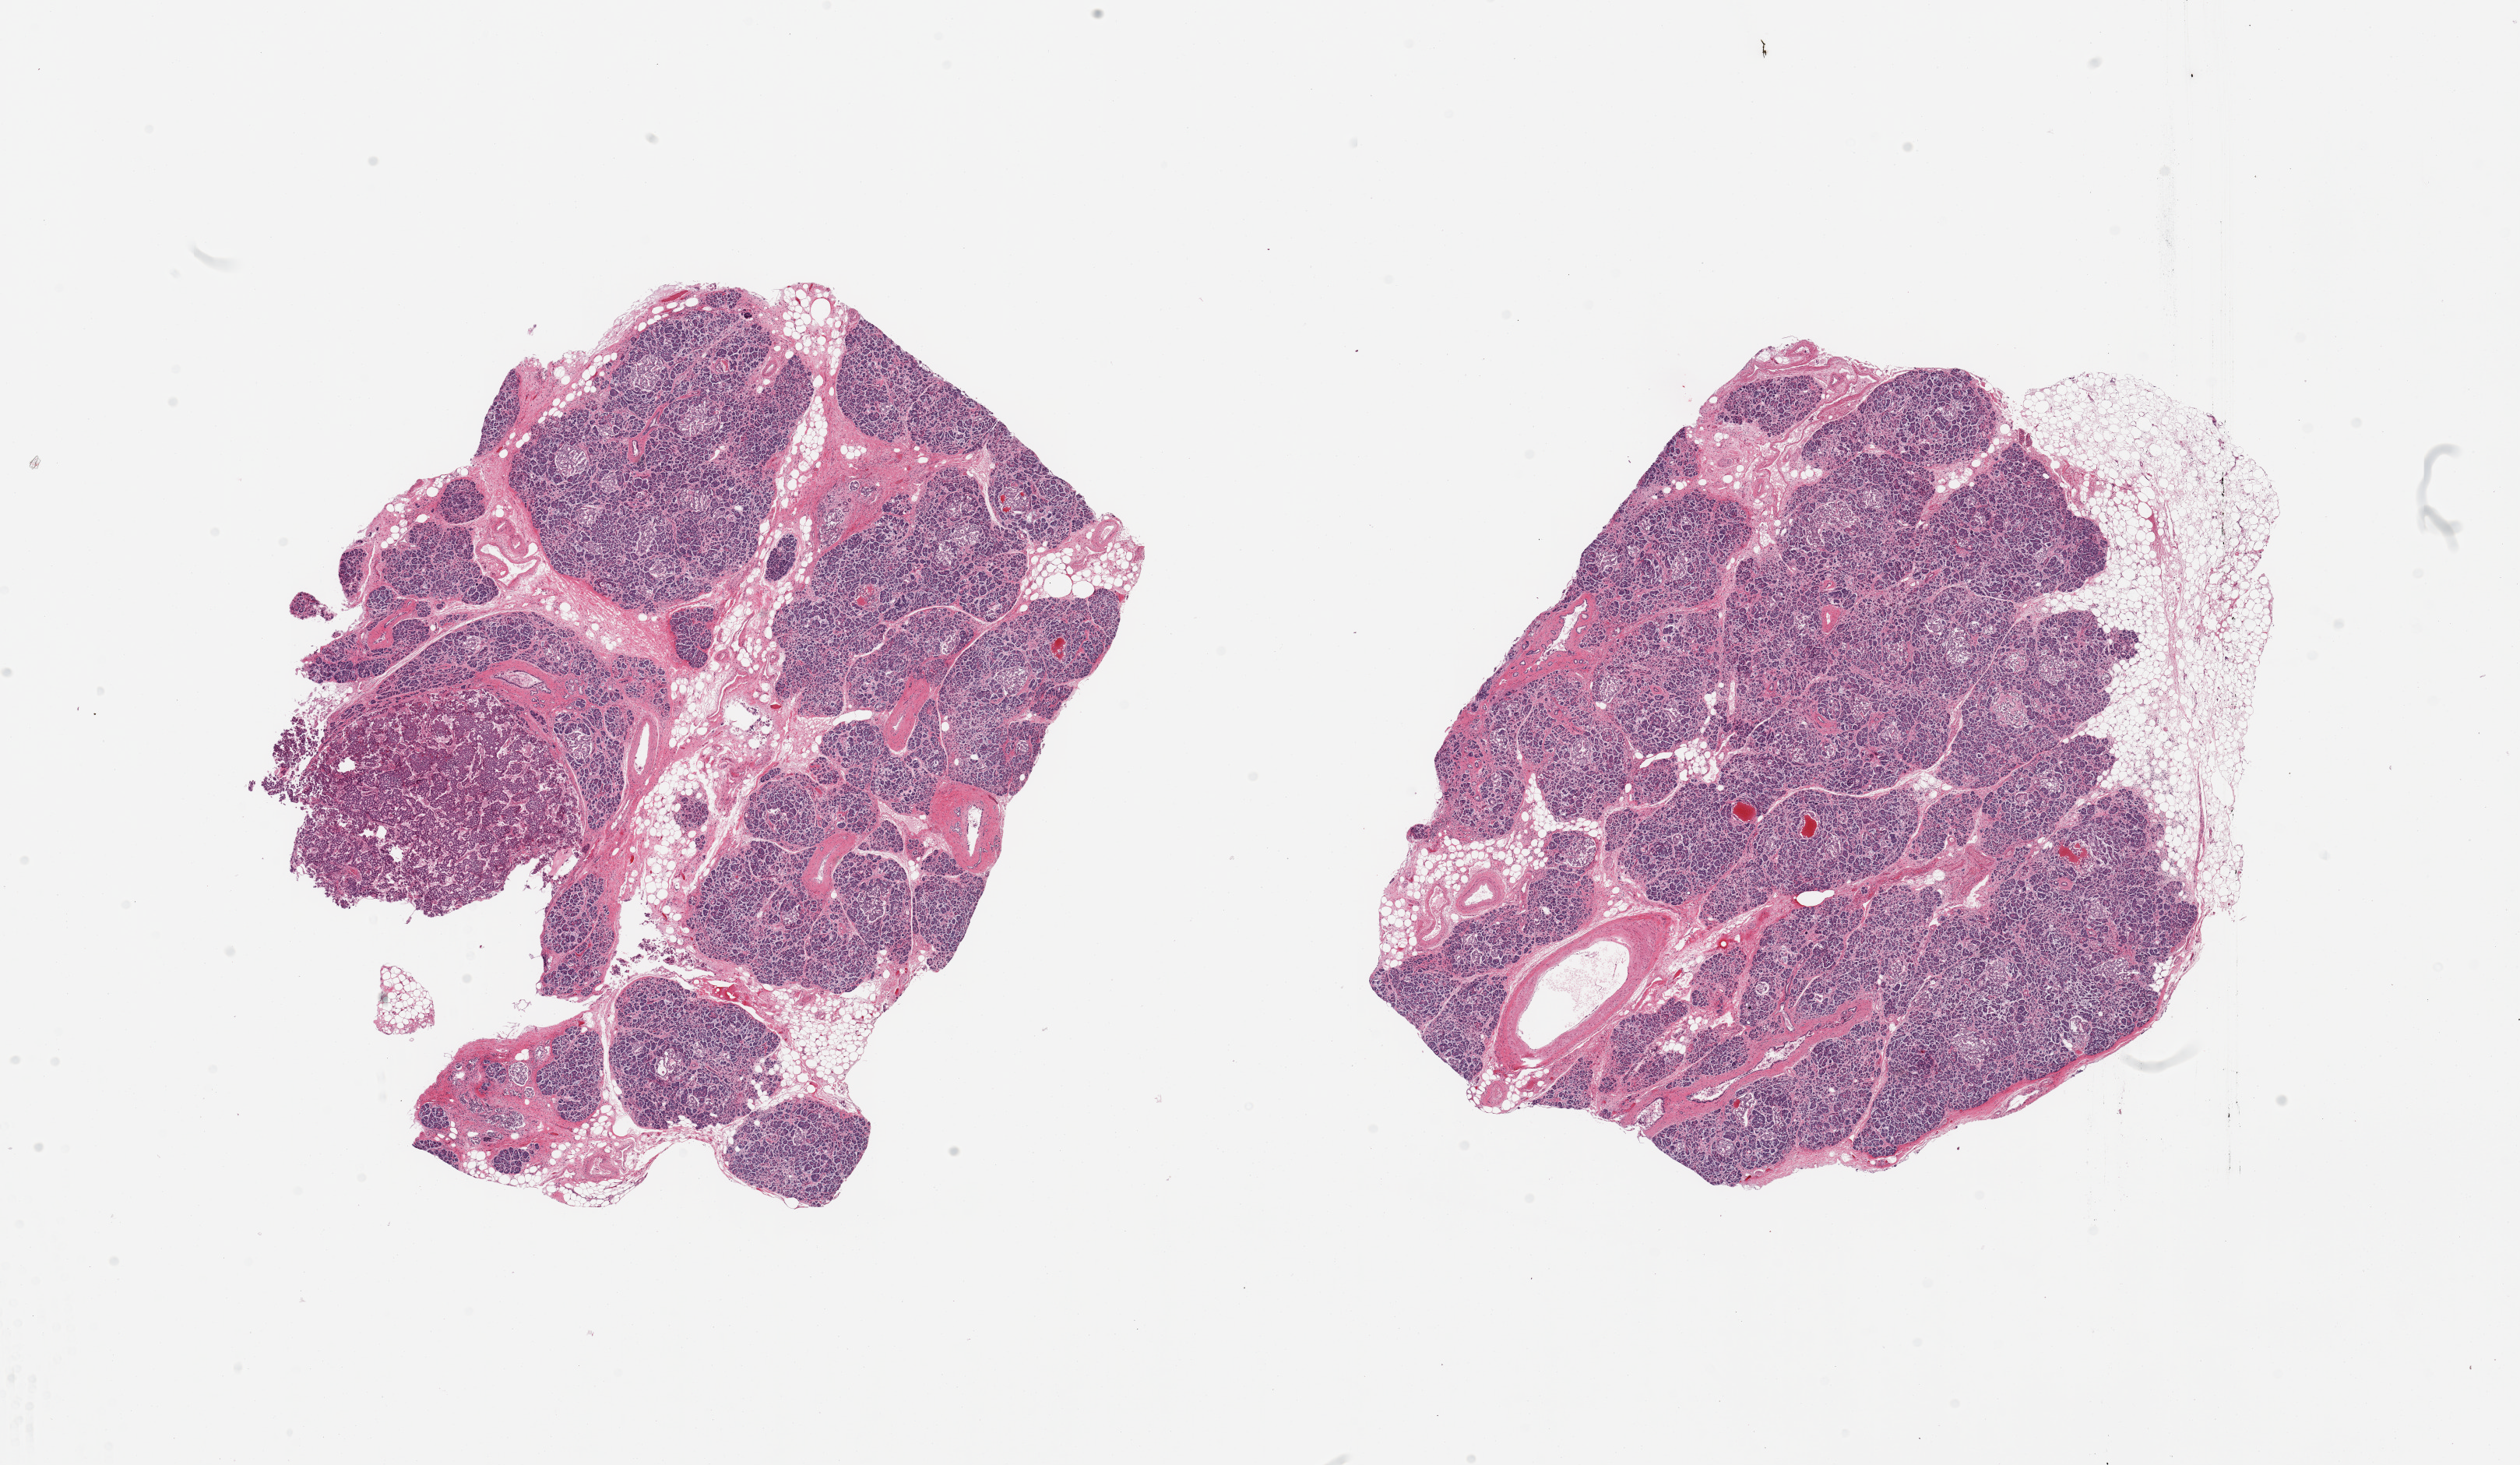
H&E whole-slide image — a low-resolution overview of the entire scanned area, about 25.6 x 14.9 mm. PAXgene-fixed paraffin-embedded (PFPE) section. Section of pancreas (target tissue). Donor tissue sample. Female donor.
- pathologist's review note for this sample: 2 pieces, numerous well-preserved Islets; Minimal adherent fat (~10%)